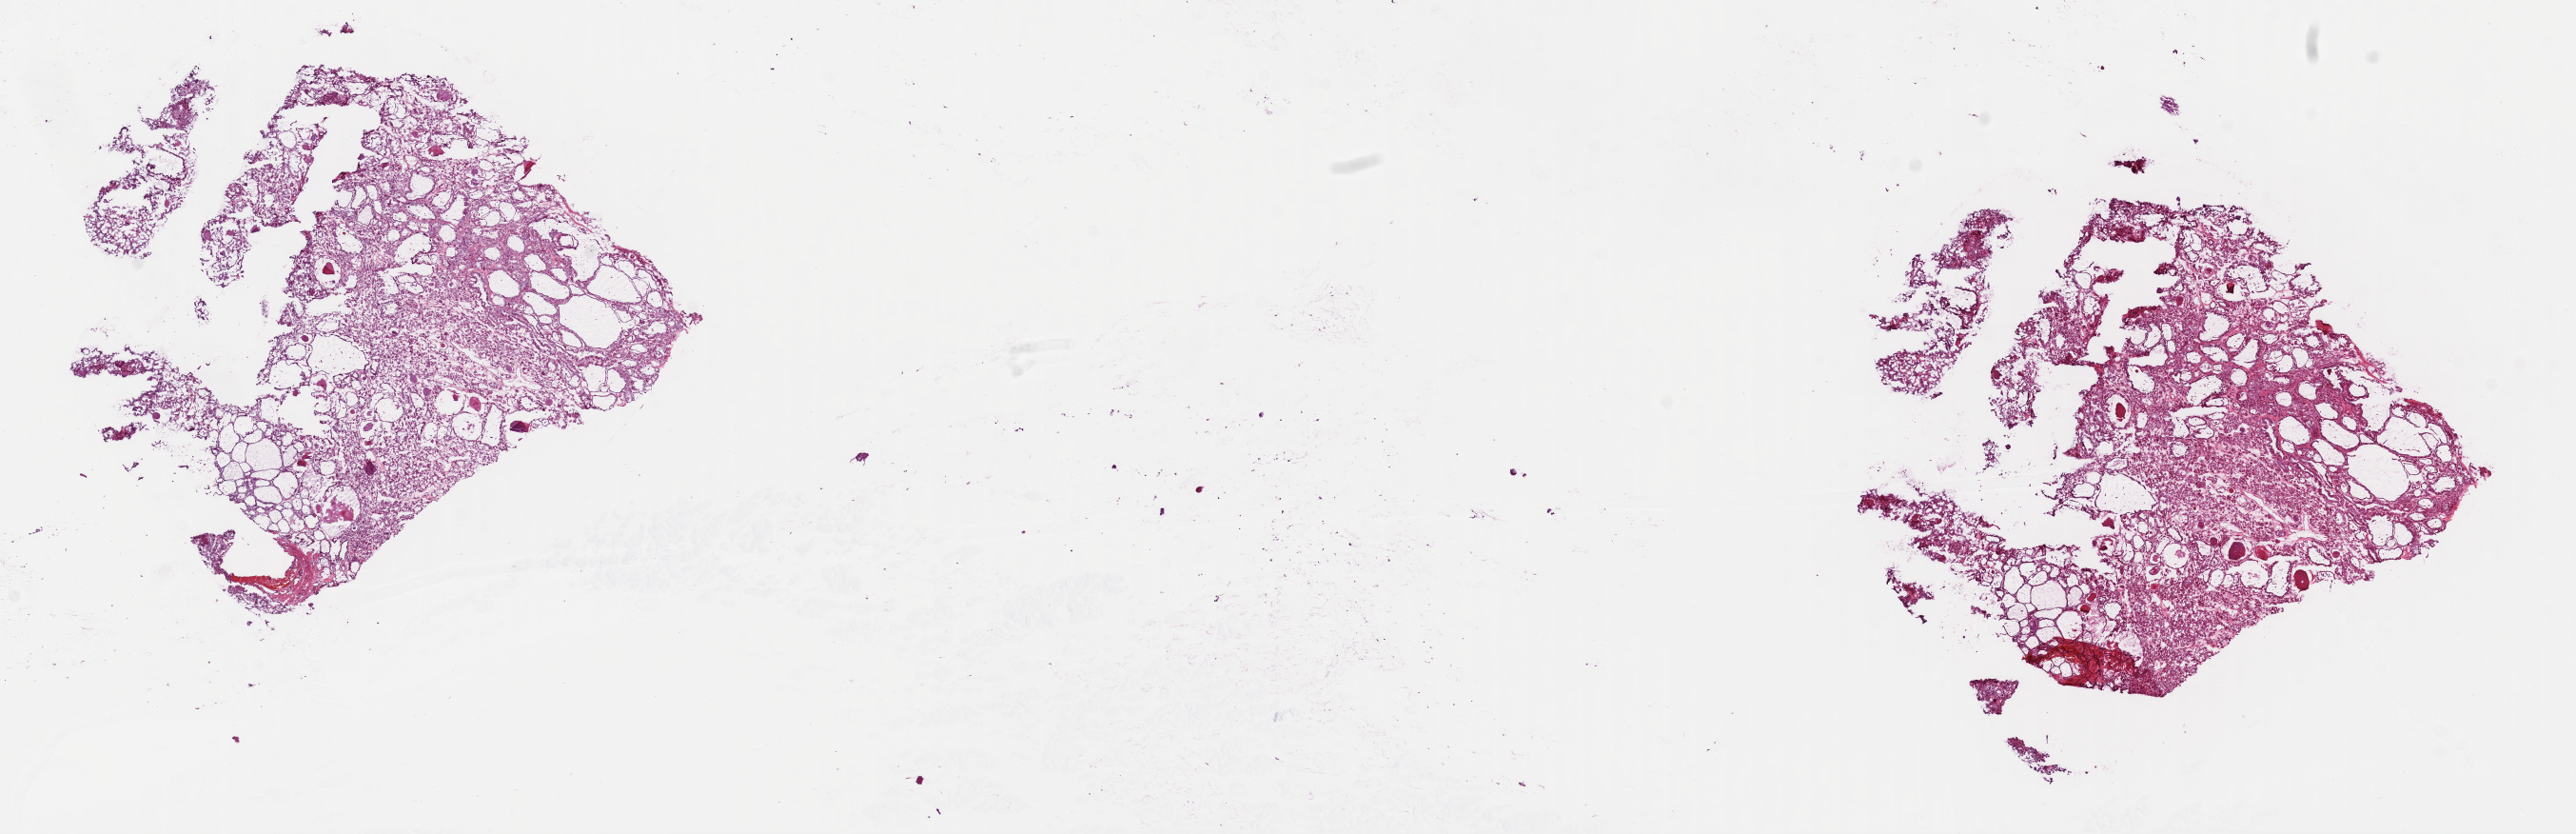
Digitized Hematoxylin and eosin (H&E) stained tissue section (whole slide) — shown as a low-resolution overview of the whole scanned area (about 21.4 x 6.9 mm, slide scanned at 40x); frozen section from the top of the tissue portion; thyroid, primary tumour sample. Female, age 64 years at initial diagnosis. Pathologist review of this section (percent, as recorded): tumour cells 80%, tumour nuclei 80%, normal cells 0%, stromal cells 20%, necrosis 0%. Infiltration values recorded for this section: lymphocyte infiltration 2%, monocyte infiltration 0%, neutrophil infiltration 0%.
* AJCC pathologic stage: II (7th edition)
* laterality: left
* lymph nodes positive (case pathology): 0 of 1 examined
* diagnosis: Papillary carcinoma, follicular variant (thyroid gland)